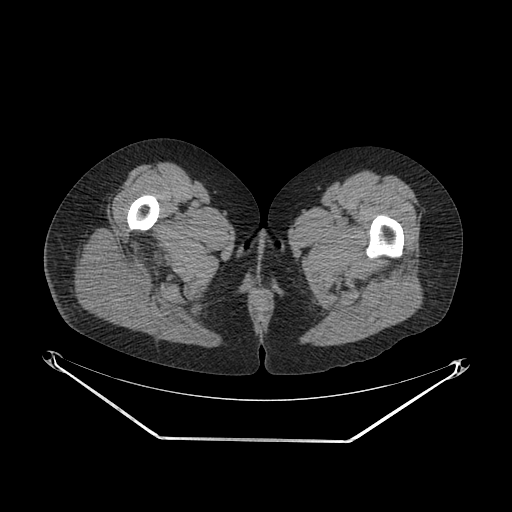
CT of an extremity soft-tissue mass (from a PET/CT study), one axial slice; position 28 of 267 along the scan axis; soft-tissue window (W 400 / L 40 HU); 3.75 mm slice thickness; 512 × 512 image matrix, field of view 500 × 500 mm. Female patient. Case-level facts recorded for this patient, not image findings: histological type: epithelioid sarcoma with vascular differentiation; site of the primary tumour: right buttock.
Structures marked on this image (expert contour drawn on MRI and transferred to this co-registered scan by the dataset authors):
- gross tumour volume (mass): box from (x=75, y=238) to (x=136, y=312) px